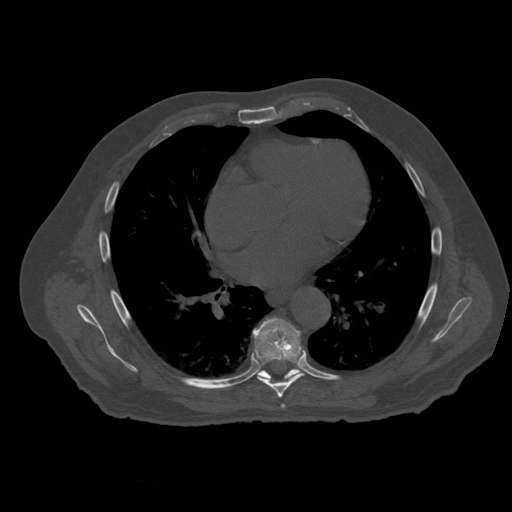
CT including the spine, one axial slice. Slice 354 of 399 in the series (ordered by position). Reconstruction kernel STANDARD. Bone window (W 1800 / L 400 HU). 512 × 512 image matrix, field of view 407 × 407 mm. Patient age 73 years. Case-level facts recorded for this patient, not image findings: primary cancer: prostate; vertebrae with lytic lesions (as recorded): L2.
Annotated regions visible in this slice (semi-automatically segmented with operator editing):
- T6 vertebra: box from (x=281, y=405) to (x=285, y=408) px
- T7 vertebra: (x=253, y=319)–(x=305, y=398)
- T8 vertebra: (x=259, y=369)–(x=300, y=380)